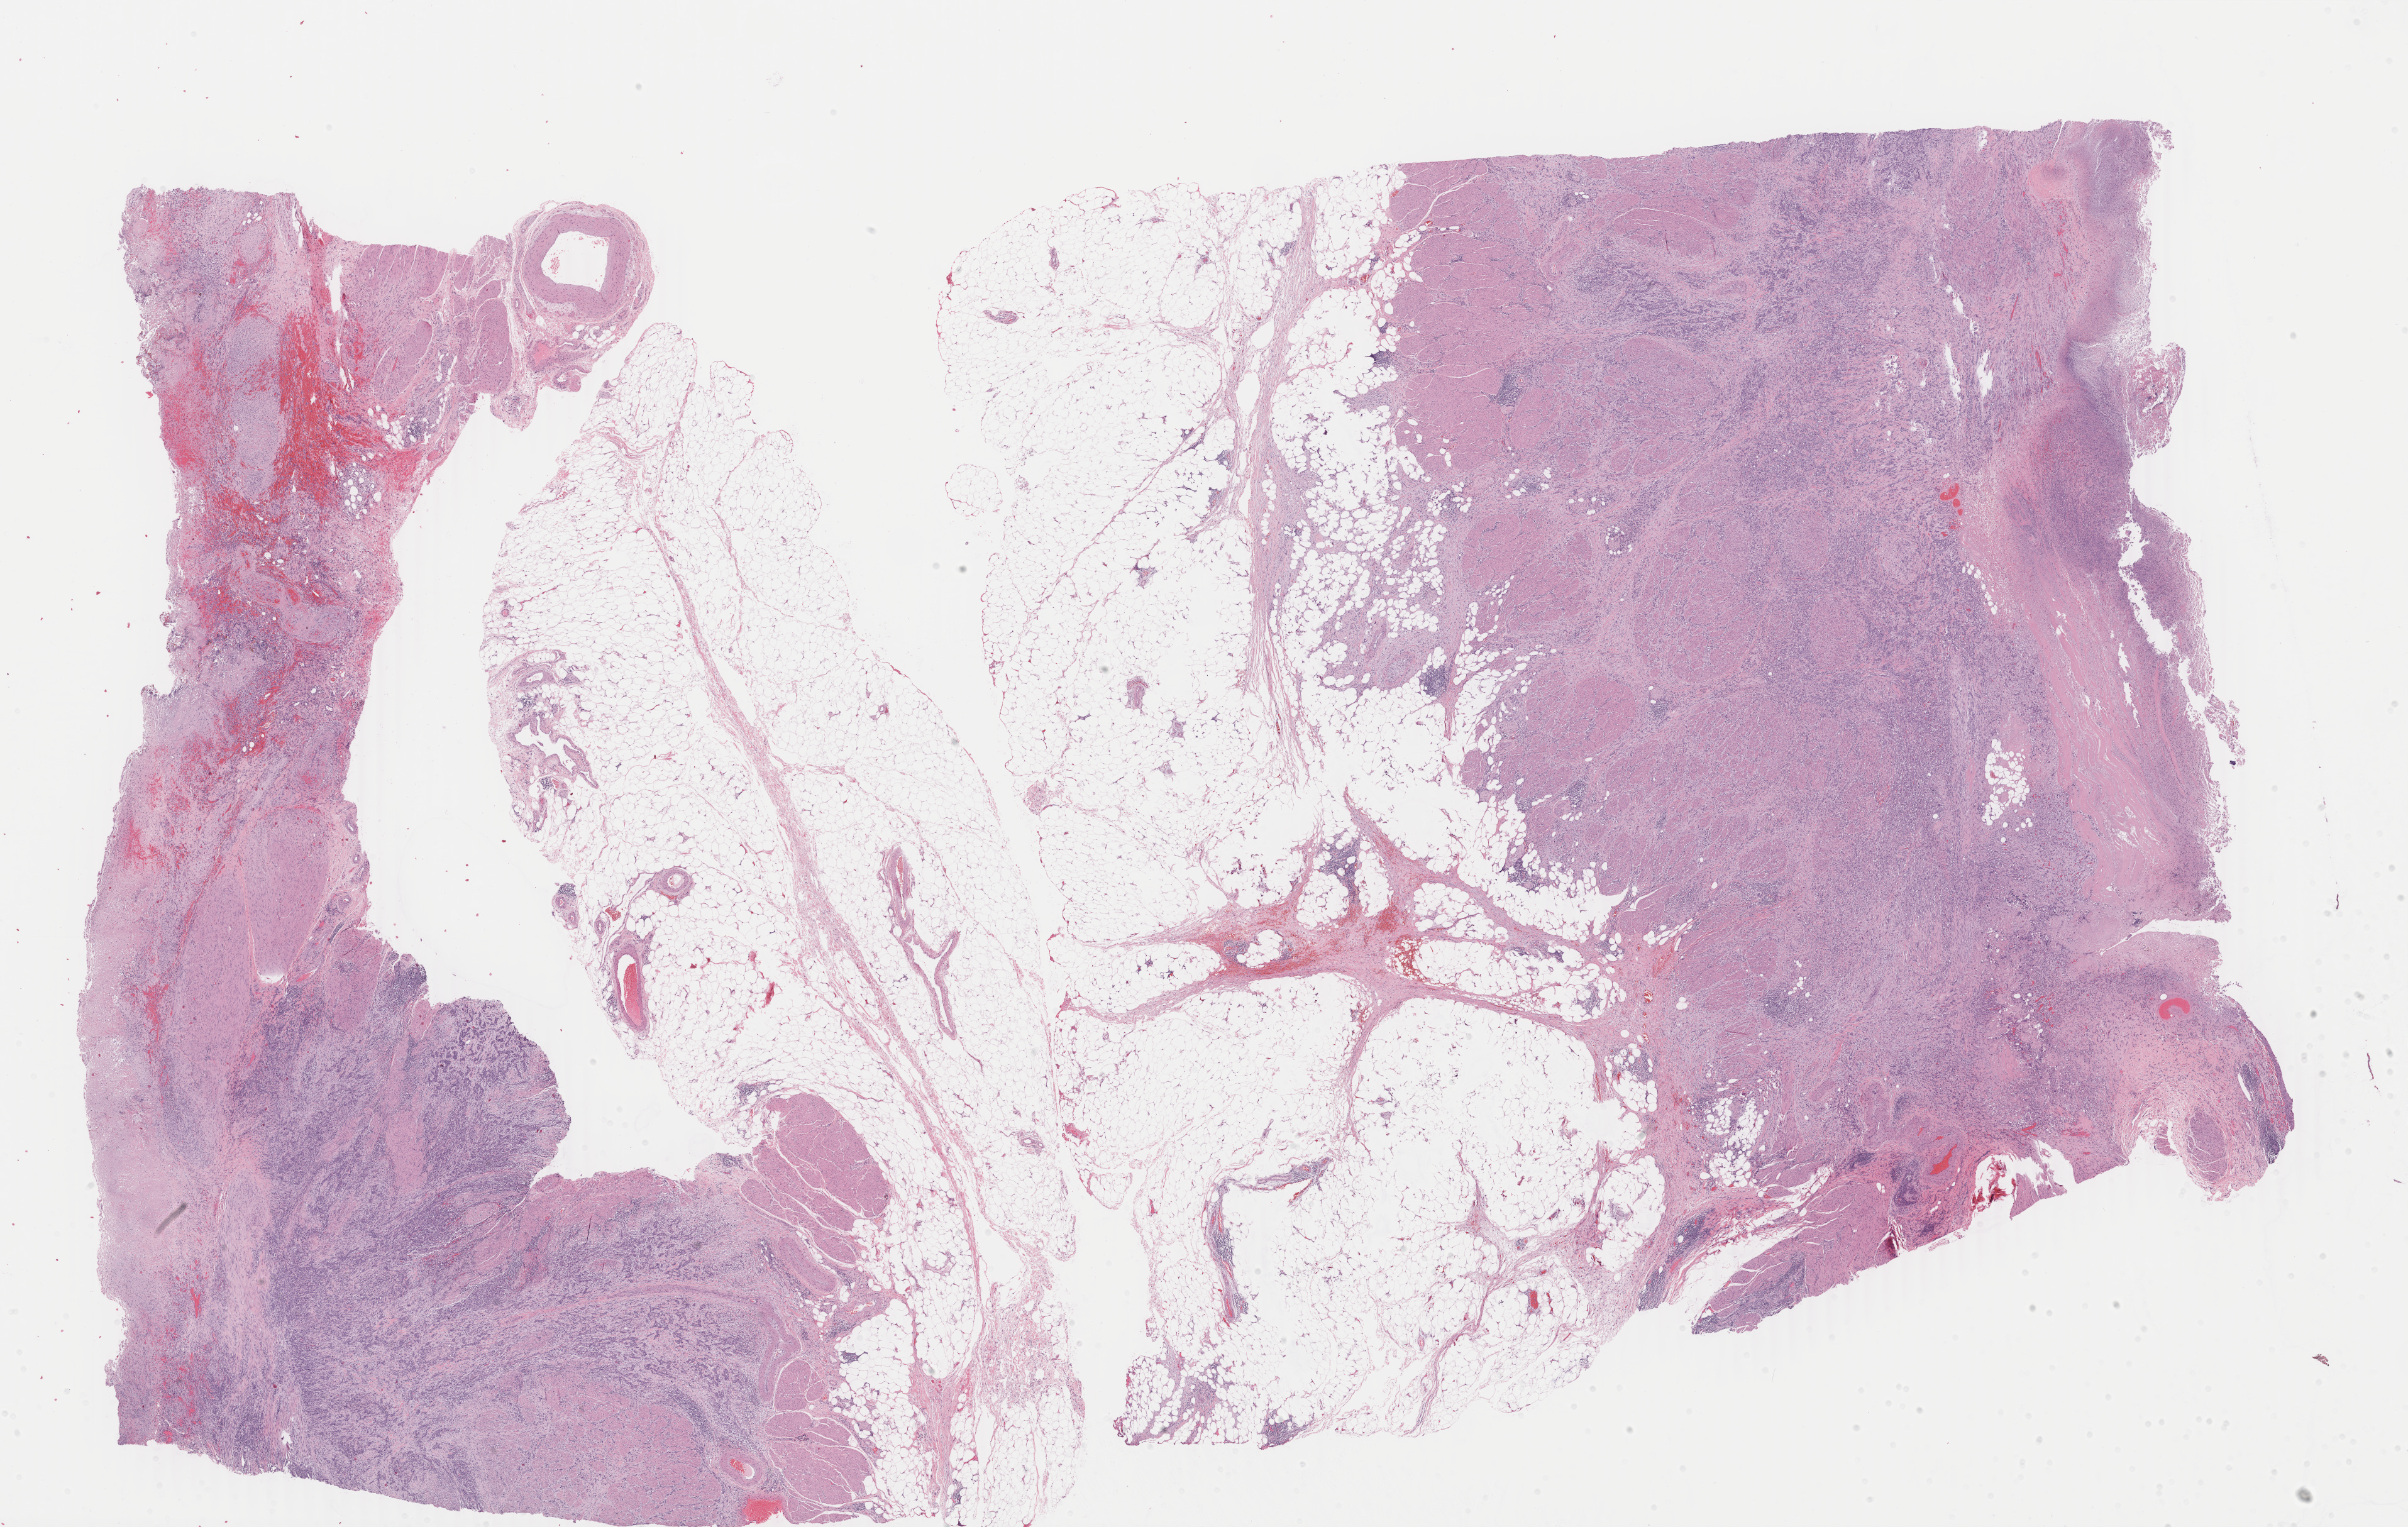
H&E-stained whole-slide image, a low-resolution overview of the entire scanned area, about 30.5 x 19.3 mm (from a 40x scan). Formalin-fixed paraffin-embedded (FFPE) diagnostic section. Primary tumour sample from the bladder. Patient: male, age at initial diagnosis 60 years. Histologic grade: high grade.
Lymph nodes positive (case pathology): 0 of 48 examined. AJCC pathologic stage: III (7th edition). Histologic diagnosis: Transitional cell carcinoma.